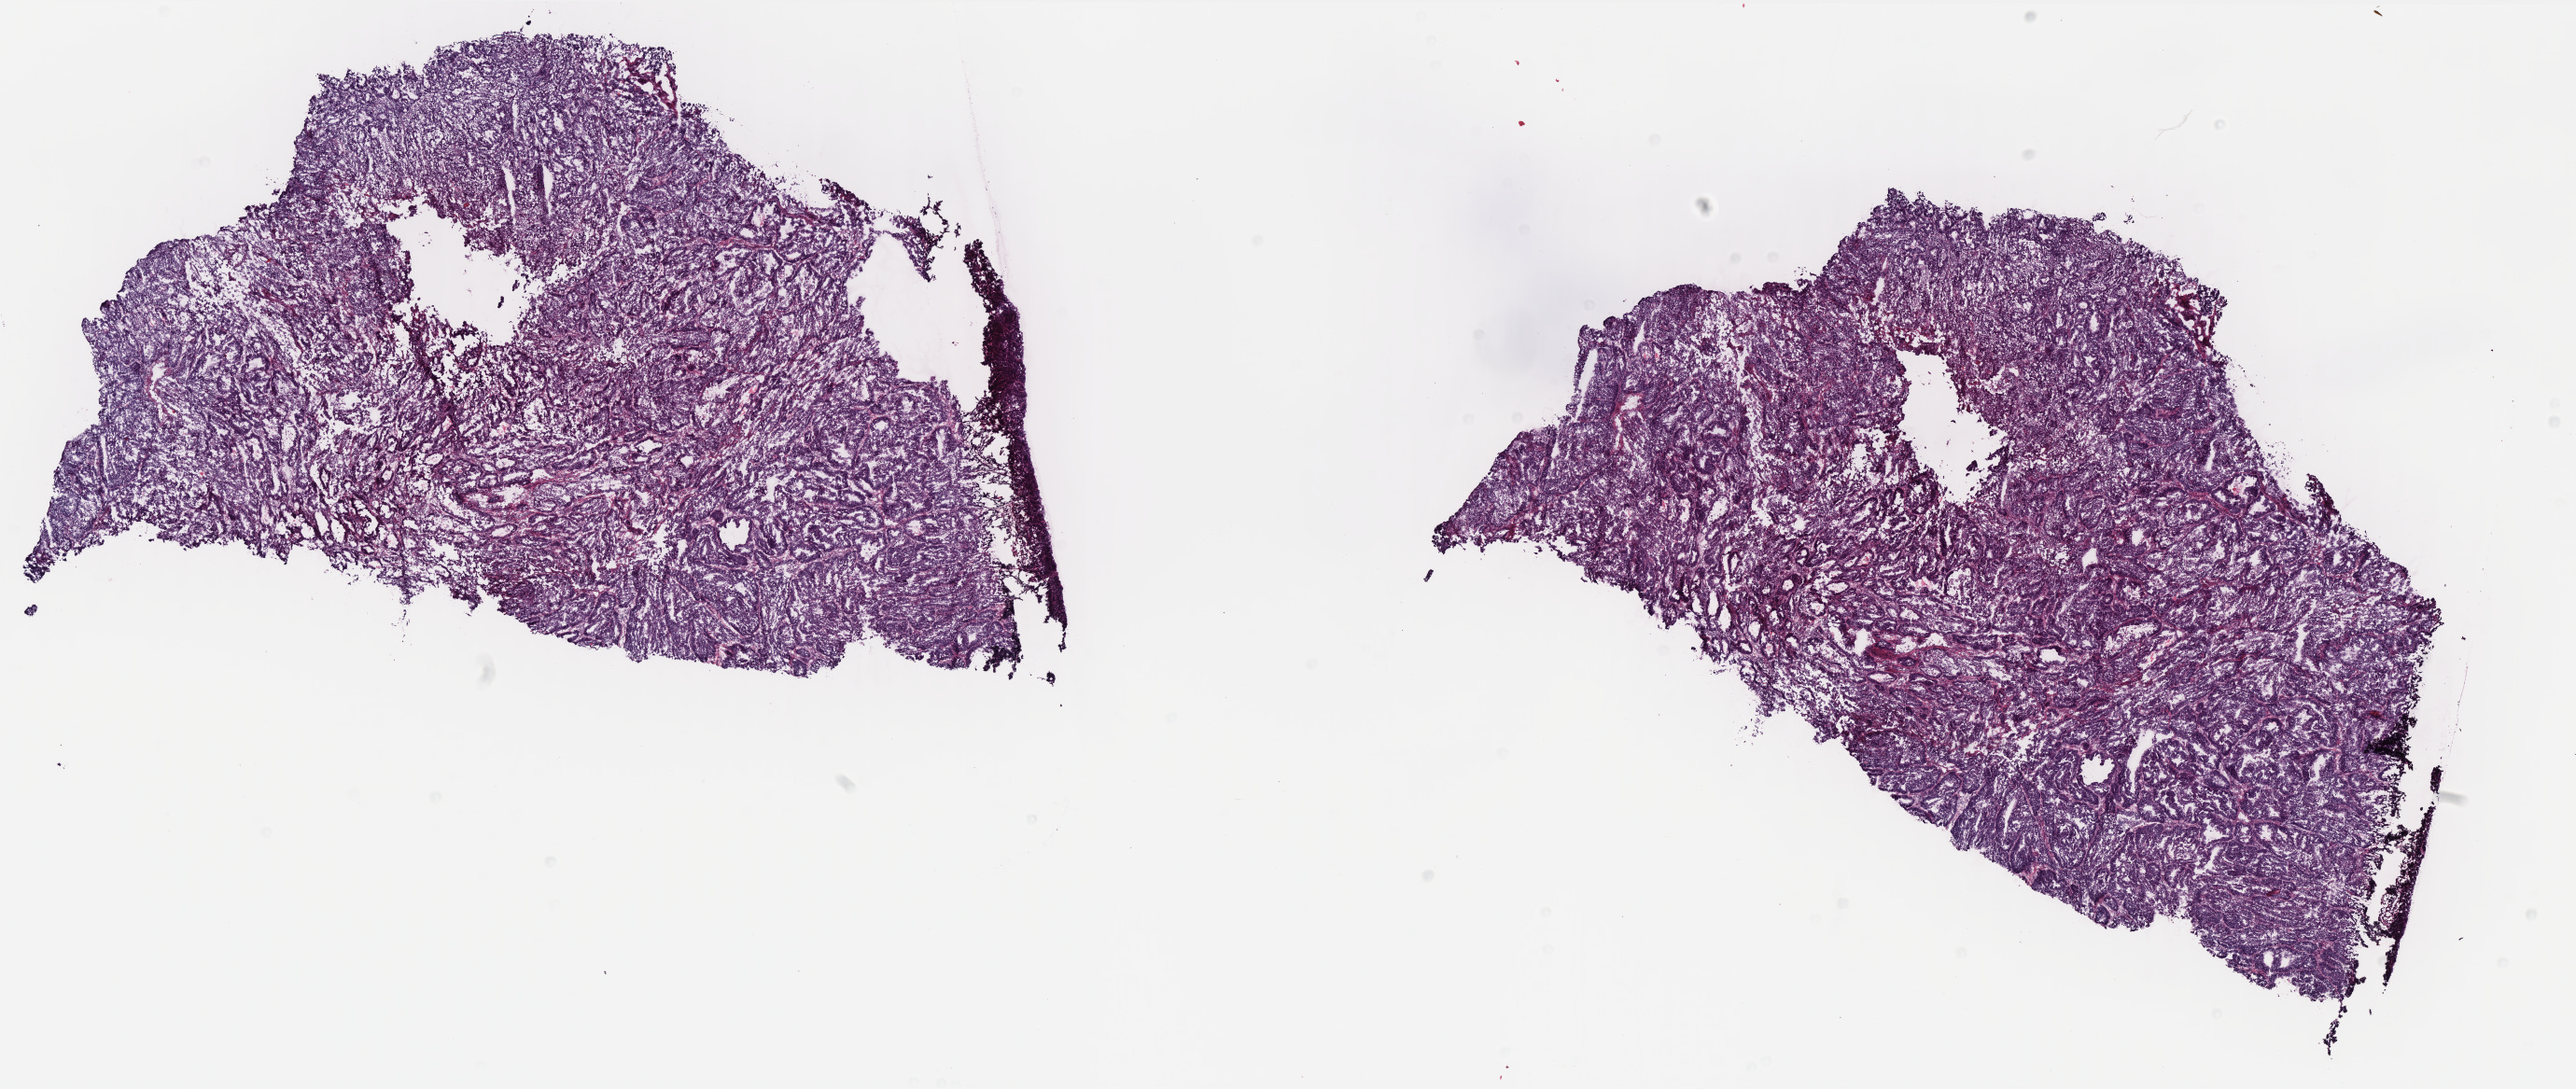
Hematoxylin and eosin (H&E) stained whole-slide image — whole scanned area (about 22.1 x 9.4 mm, from a 40x scan) shown as a low-resolution overview; frozen section from the top of the tissue portion; uterus, primary tumour sample. Female patient; age at initial diagnosis 58 years. Histologic grade: G1 (well differentiated). Slide review estimates, as recorded: tumour cells 60%, tumour nuclei 70%, normal cells 0%, stromal cells 30%, necrosis 10%. Inflammatory infiltration, as recorded: lymphocyte infiltration 25%, monocyte infiltration 20%, neutrophil infiltration 20%.
• FIGO stage: IA
• diagnosis: Endometrioid adenocarcinoma, NOS (endometrium)